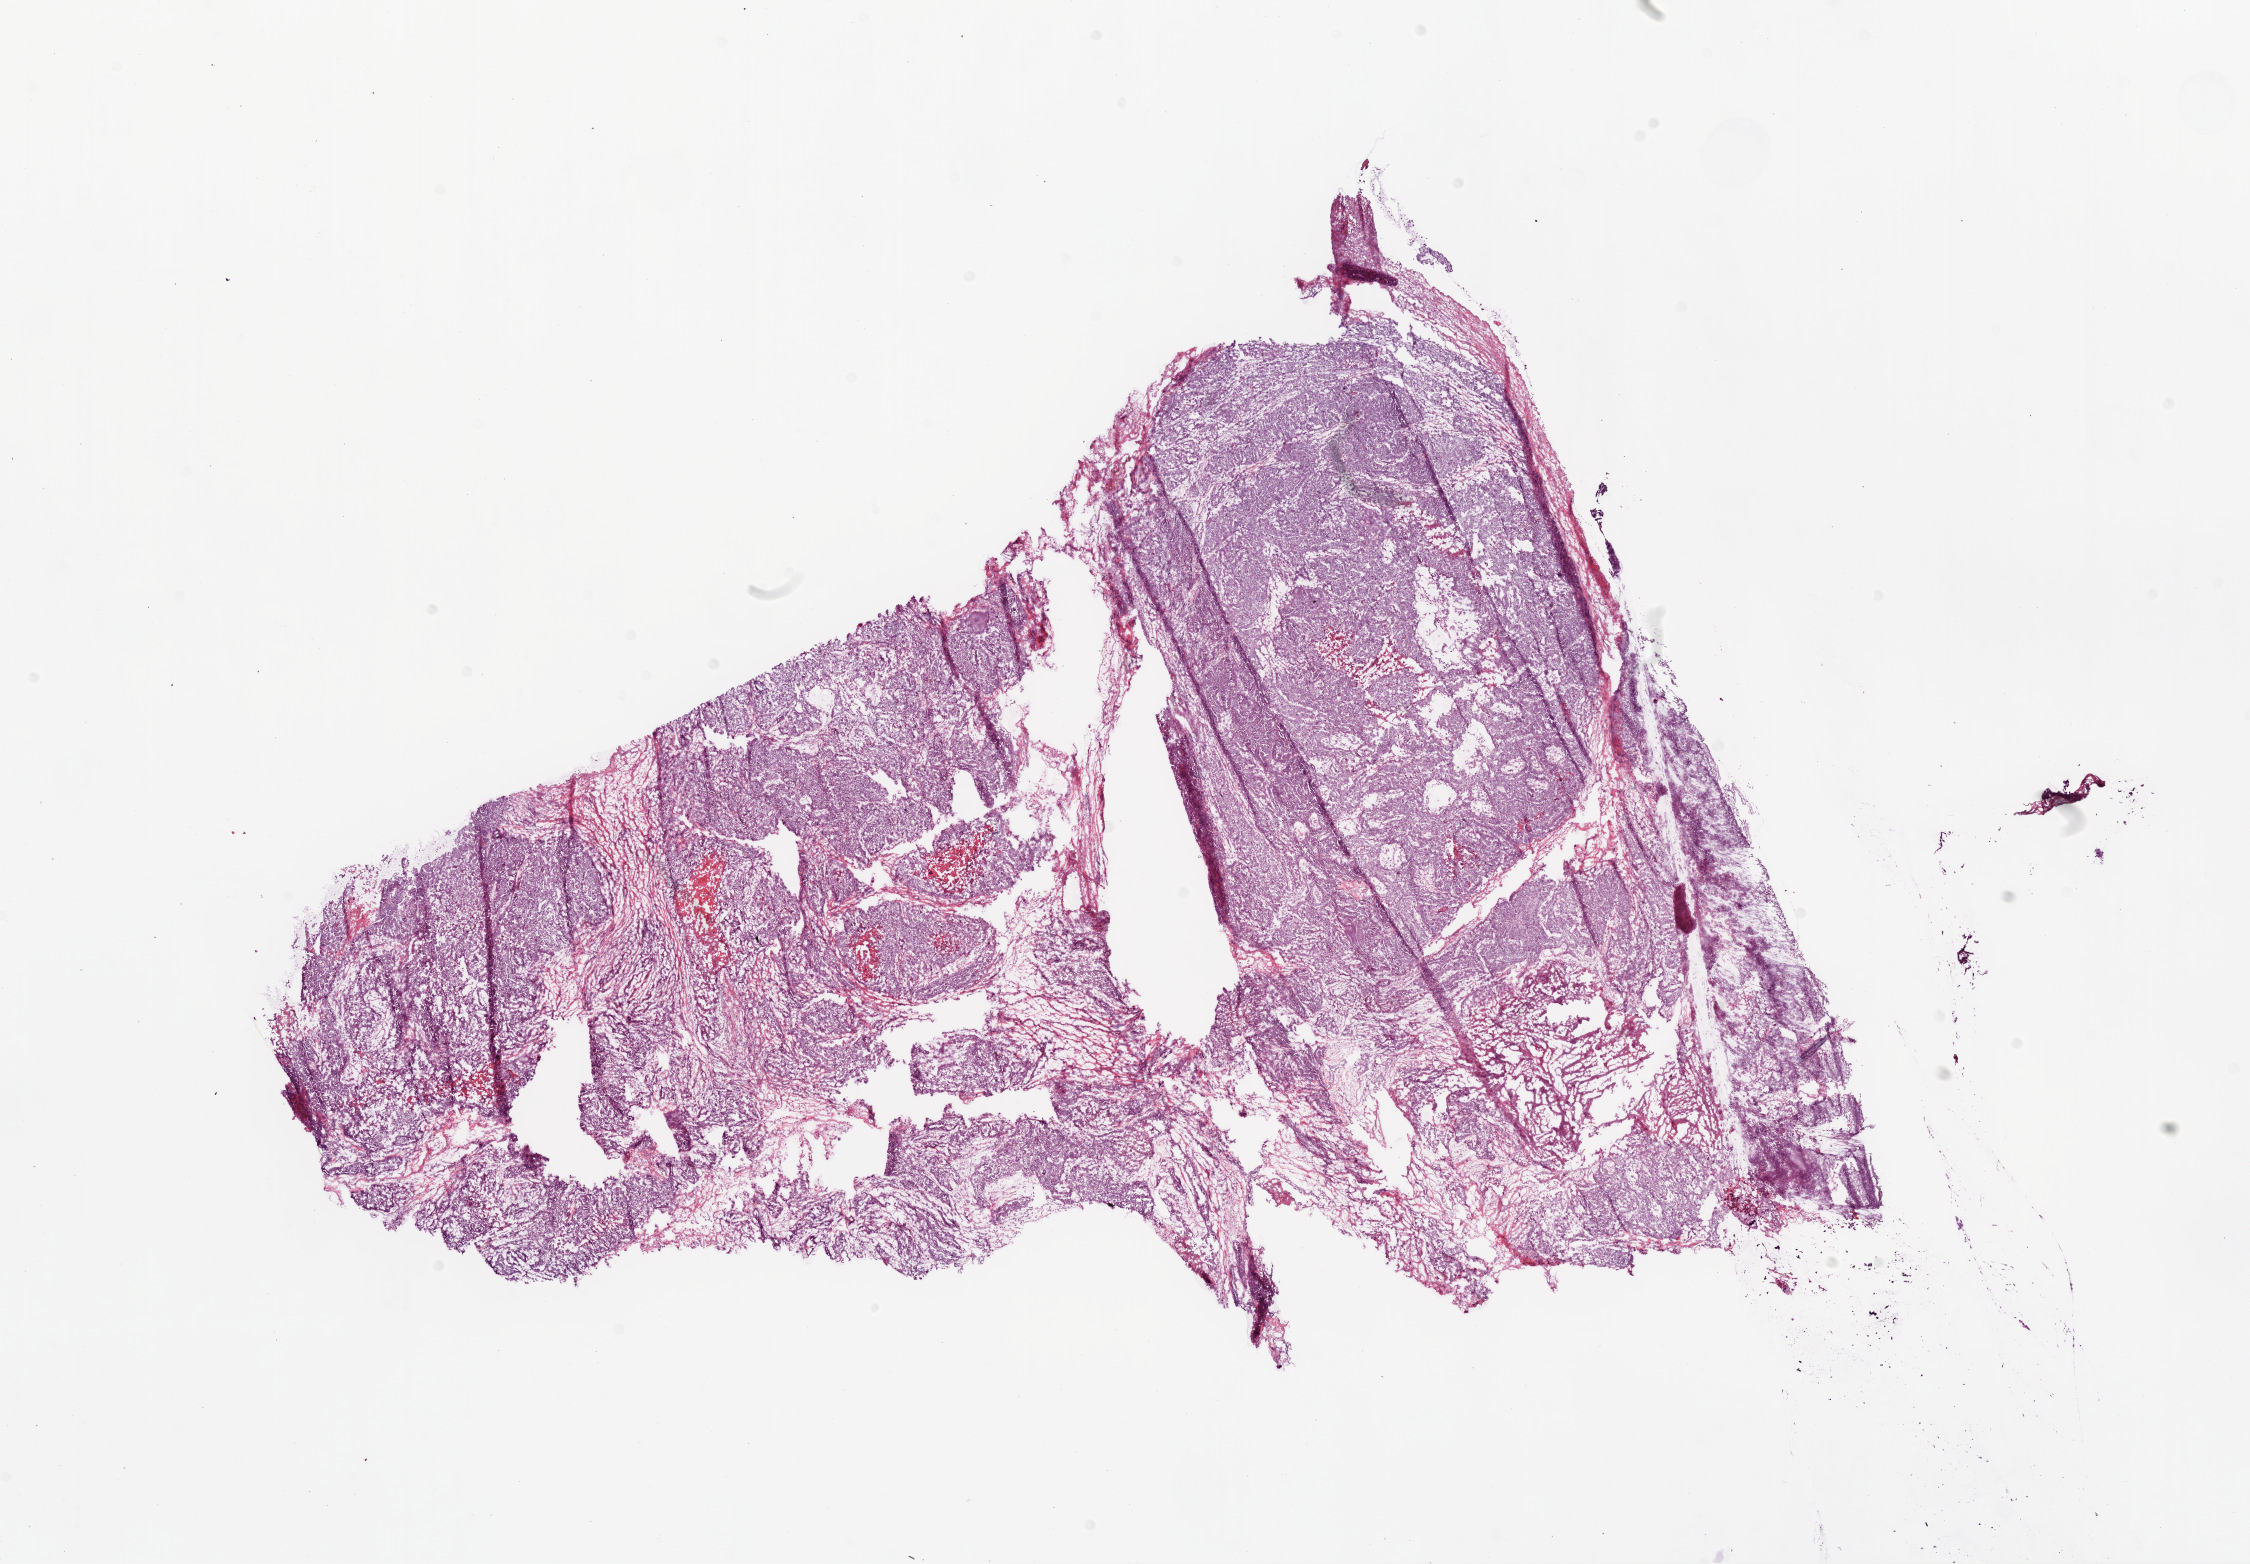
H&E-stained whole-slide image, low-resolution overview of the scanned area, about 18.1 x 12.5 mm (slide scanned at 20x), frozen section from the top of the tissue portion, sample: primary tumour, ovary. Female patient; age at initial diagnosis 81 years. Histologic grade: G2 (moderately differentiated). Pathologist review of this section (percent, as recorded): tumour cells 80%, tumour nuclei 90%, normal cells 0%, stromal cells 10%, necrosis 10%.
FIGO stage: IIC. Pathologic diagnosis: Serous cystadenocarcinoma, NOS.